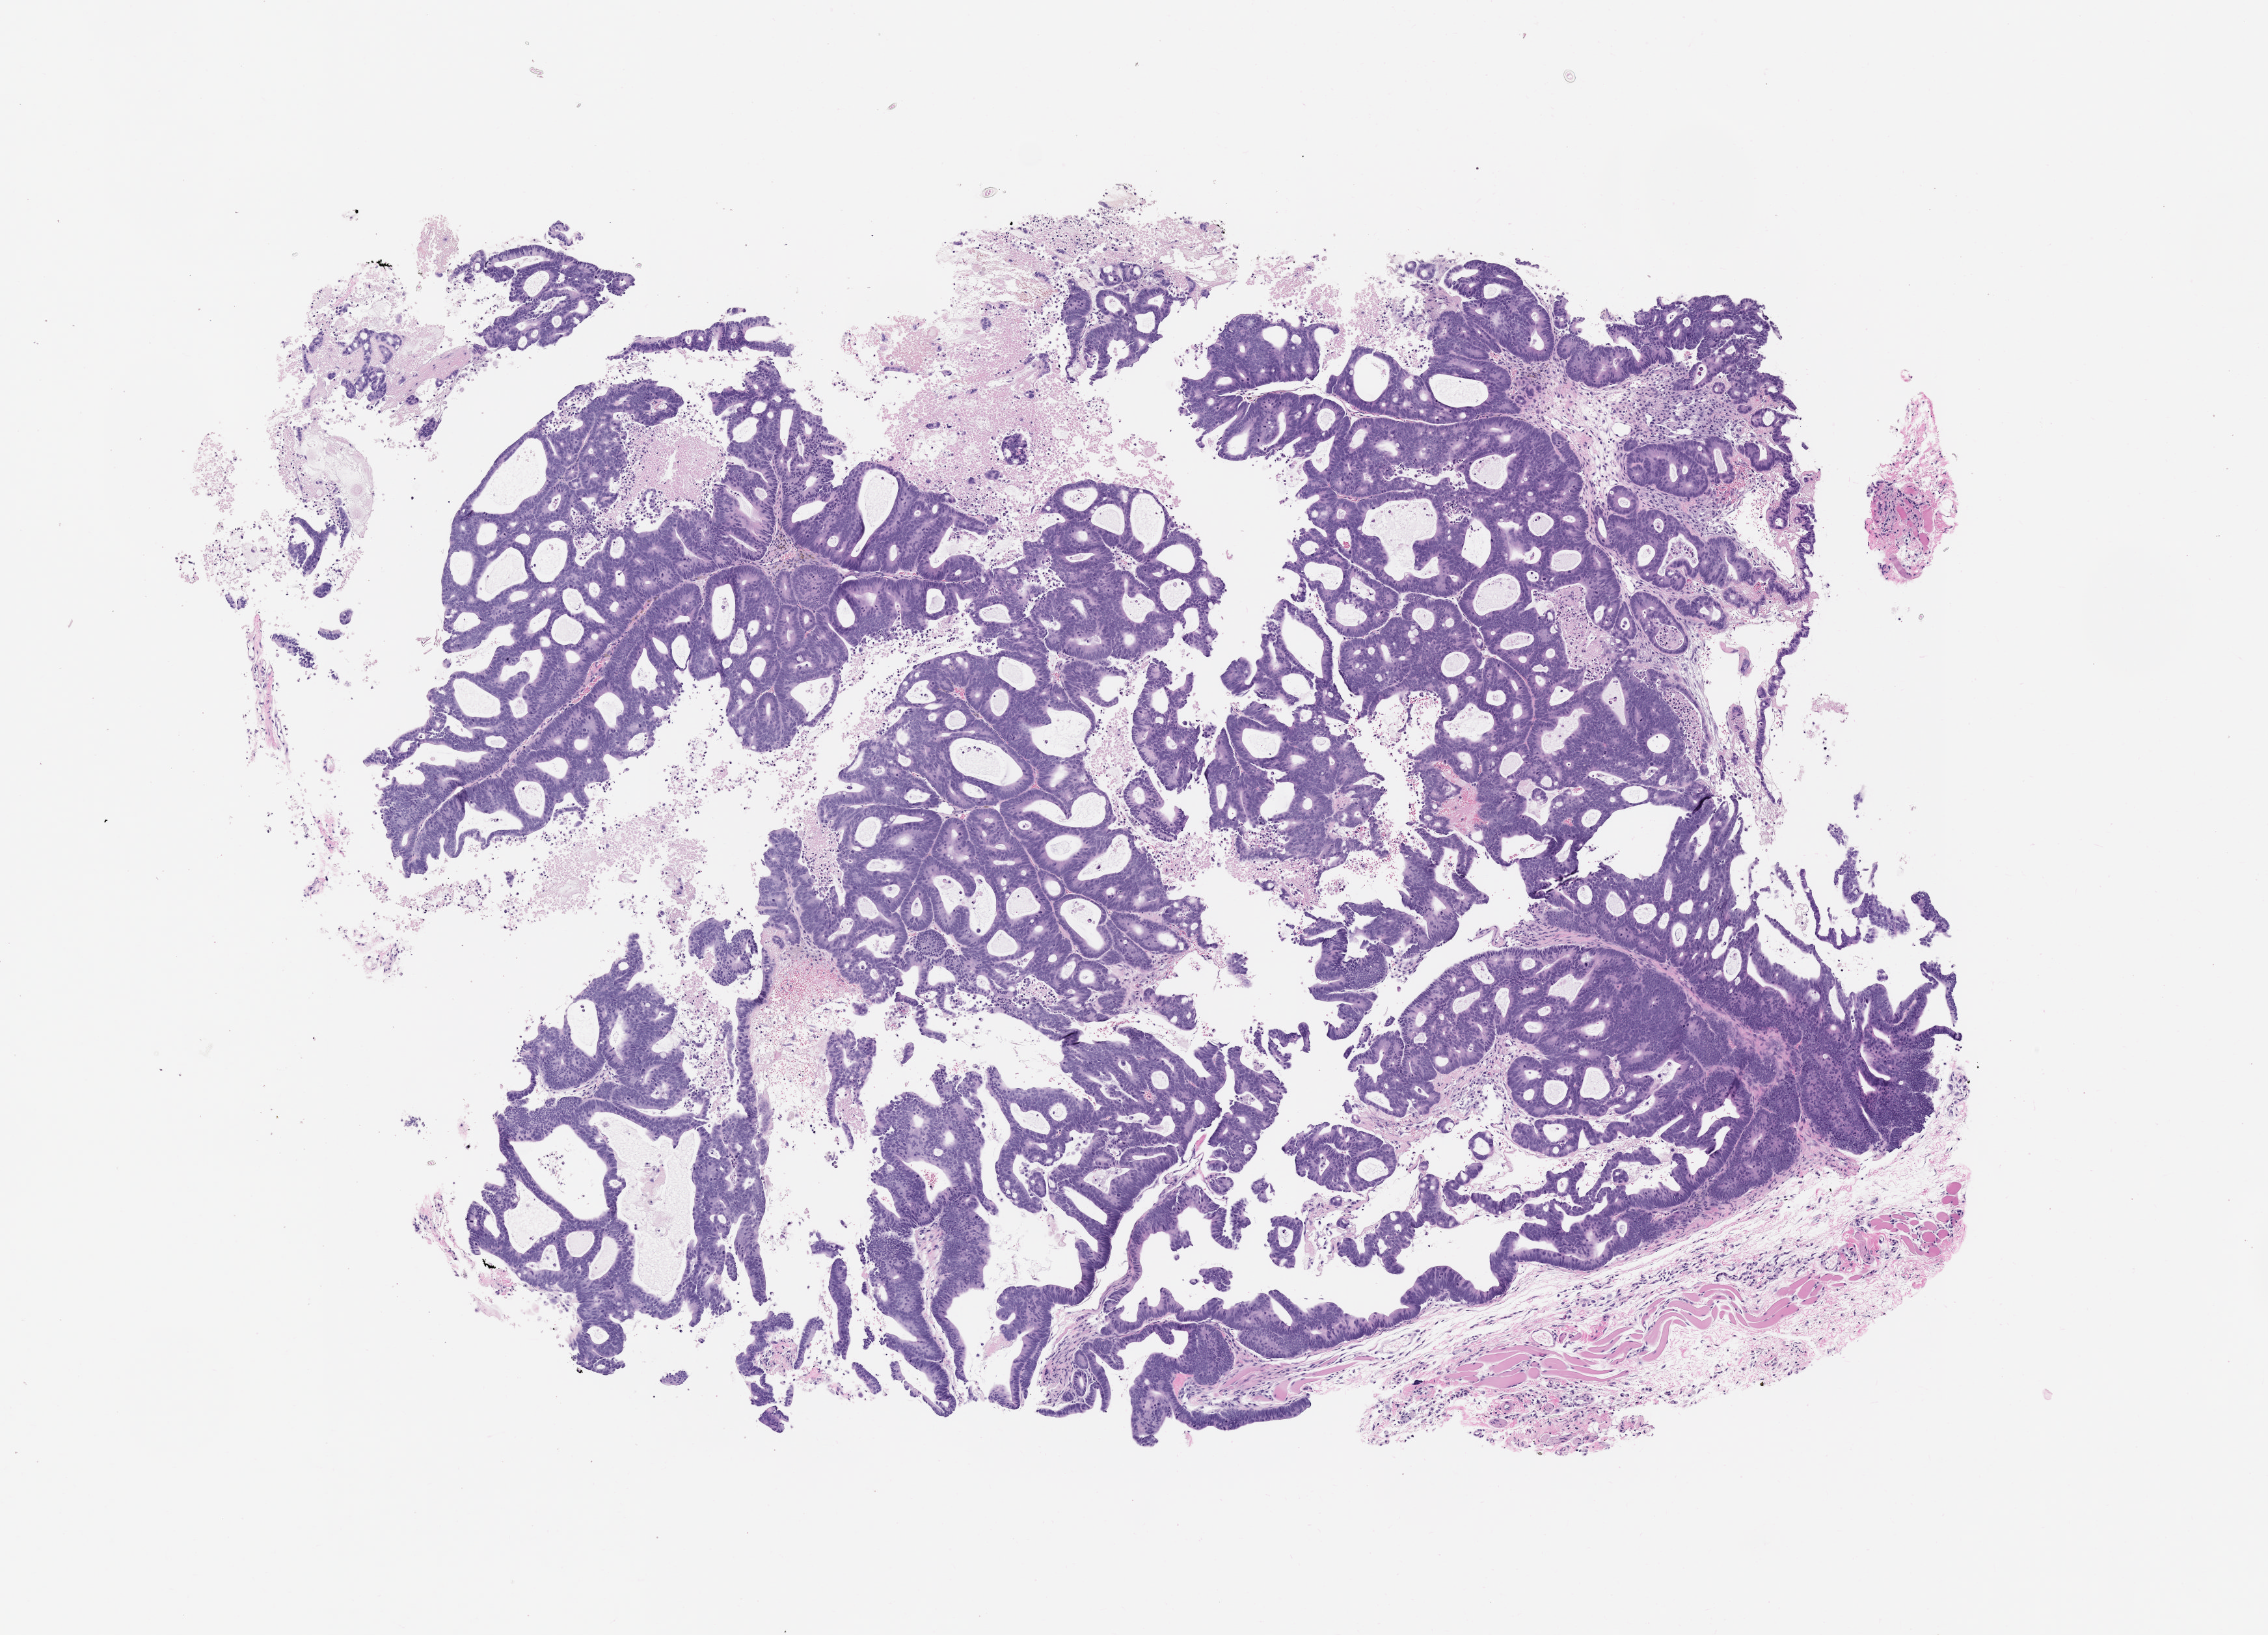
Whole-slide image, H&E: patient-derived xenograft (human tumor grown in a mouse), passage 2 — low-resolution overview of the scanned area, about 7.0 x 5.1 mm. Formalin-fixed paraffin-embedded section. Originating tumor site category: colon.
• originating patient diagnosis: Colon Adenocarcinoma